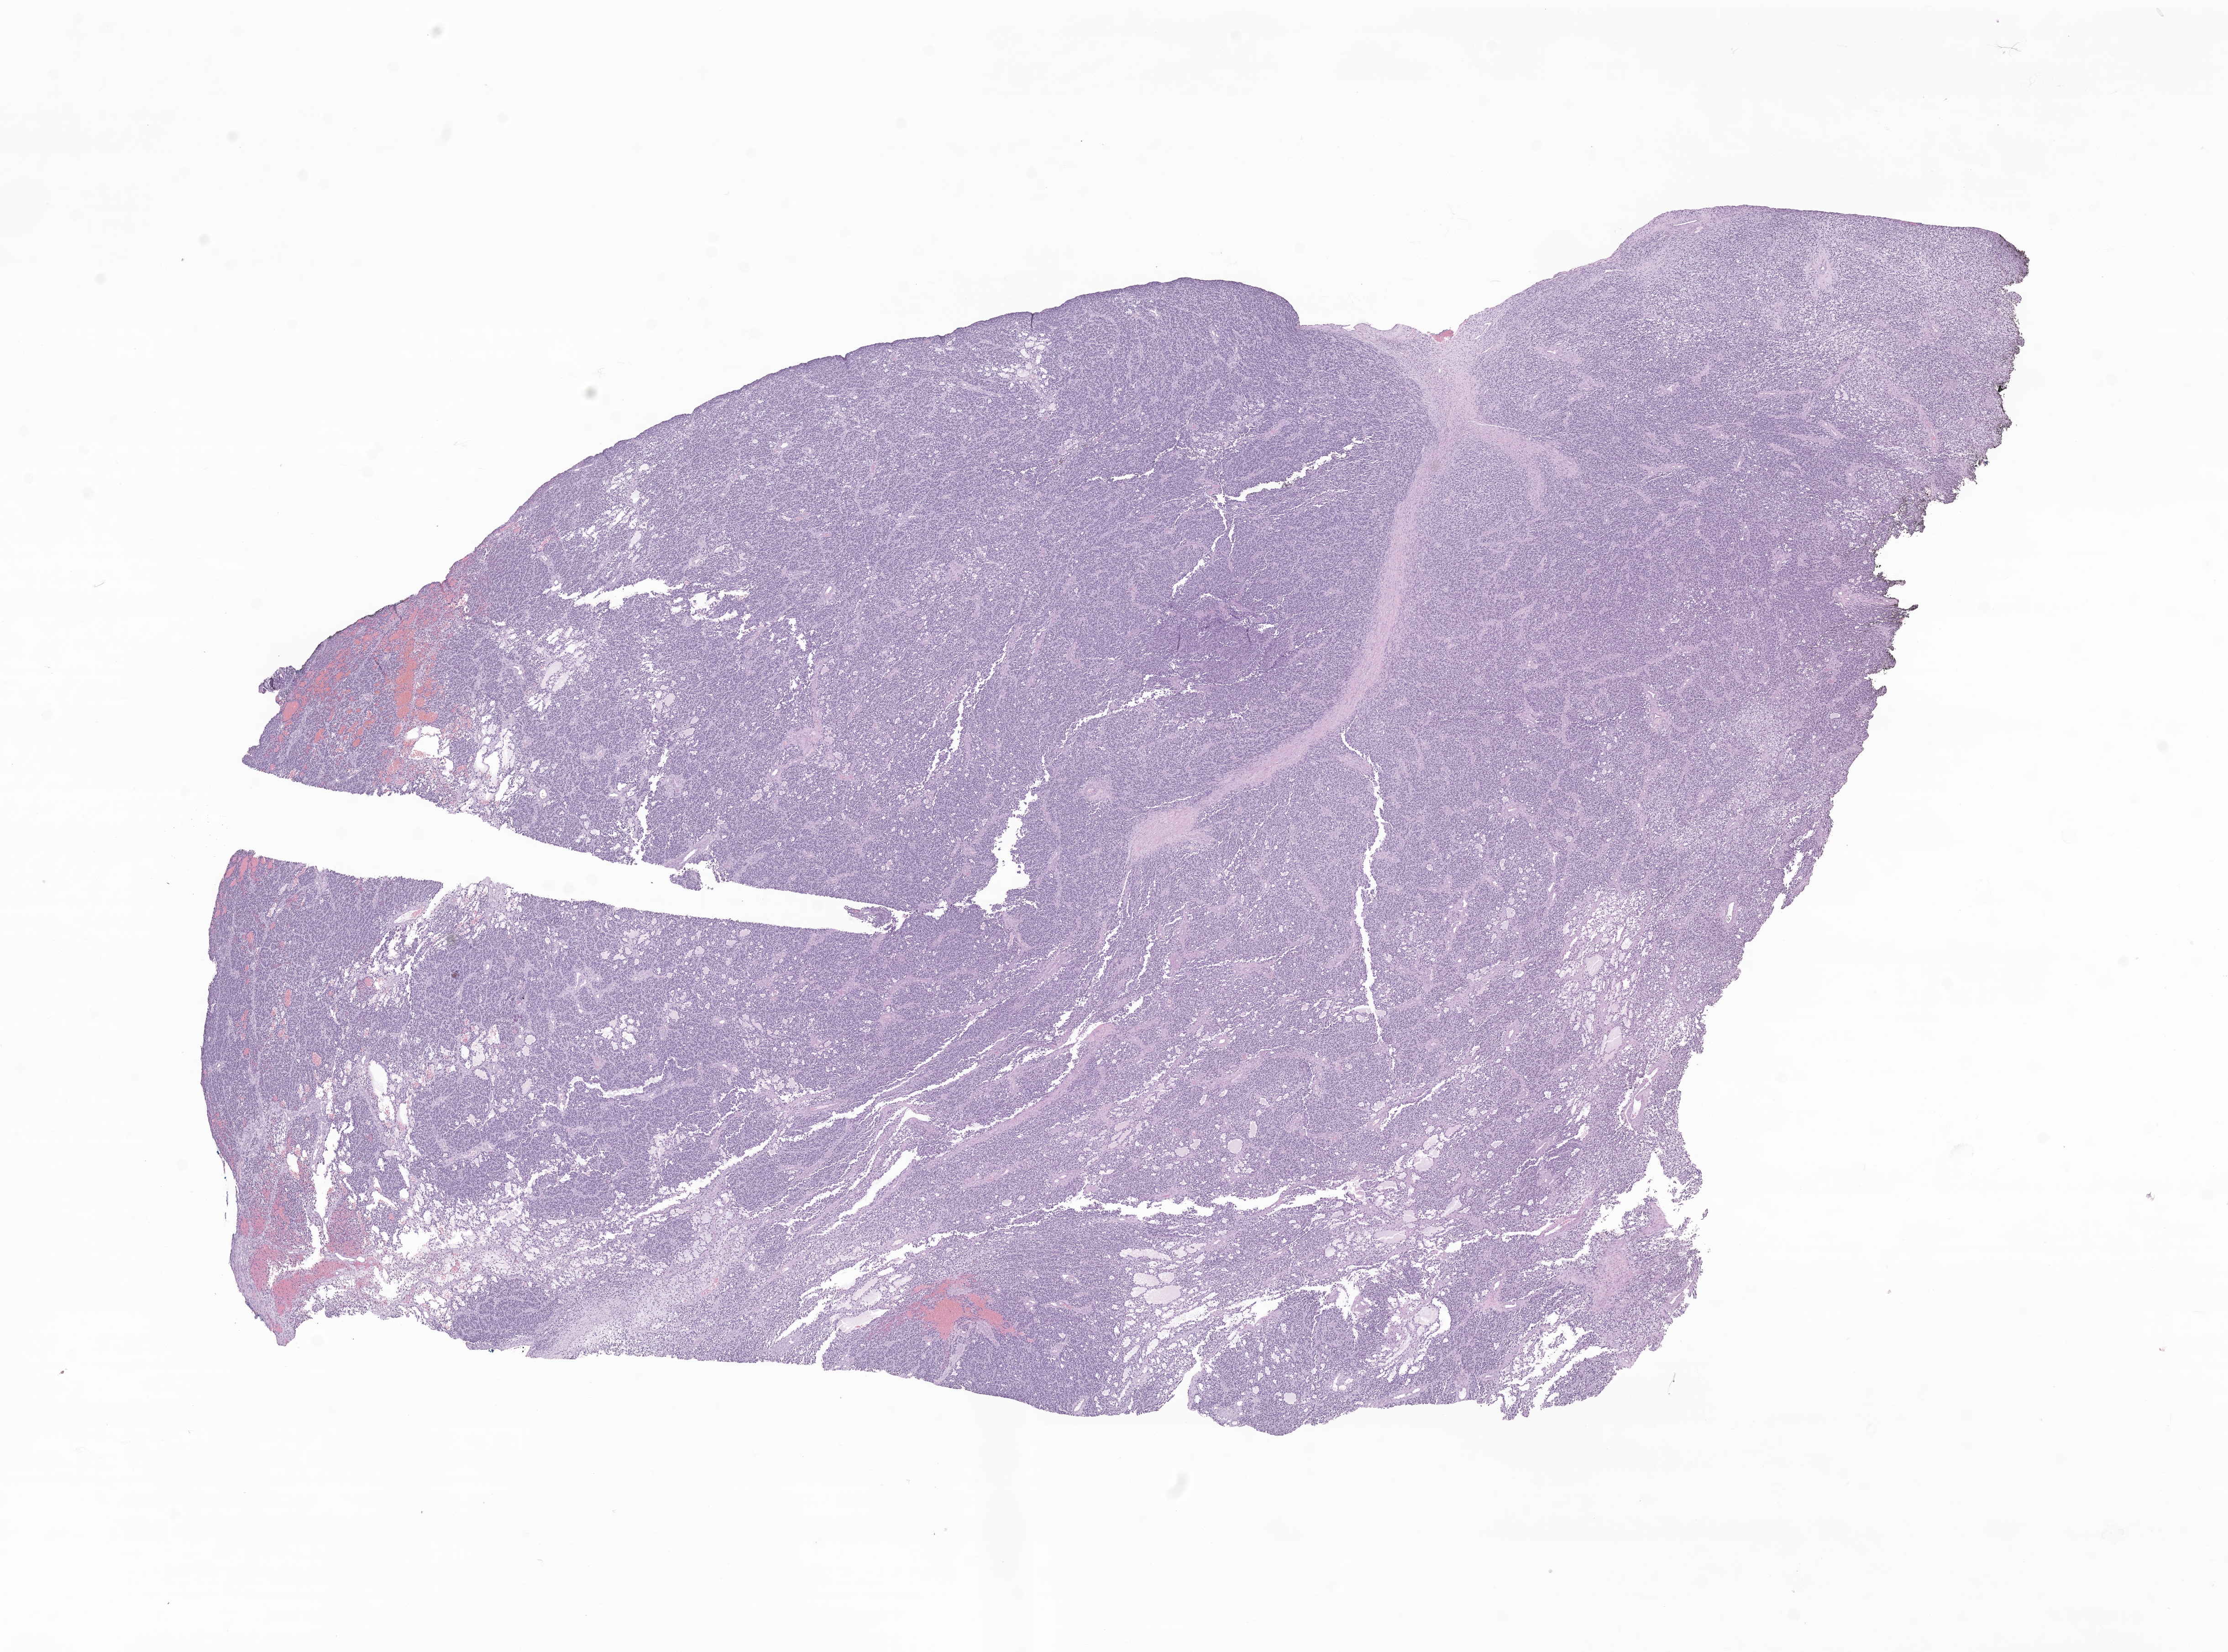
Whole-slide image, haematoxylin and eosin stain of tumor tissue from the testis, a low-resolution overview of the entire scanned area, about 20.6 x 15.3 mm, formalin-fixed paraffin-embedded section. Patient: male, age 200 months.
Recorded diagnosis: Embryonal rhabdomyosarcoma, NOS.